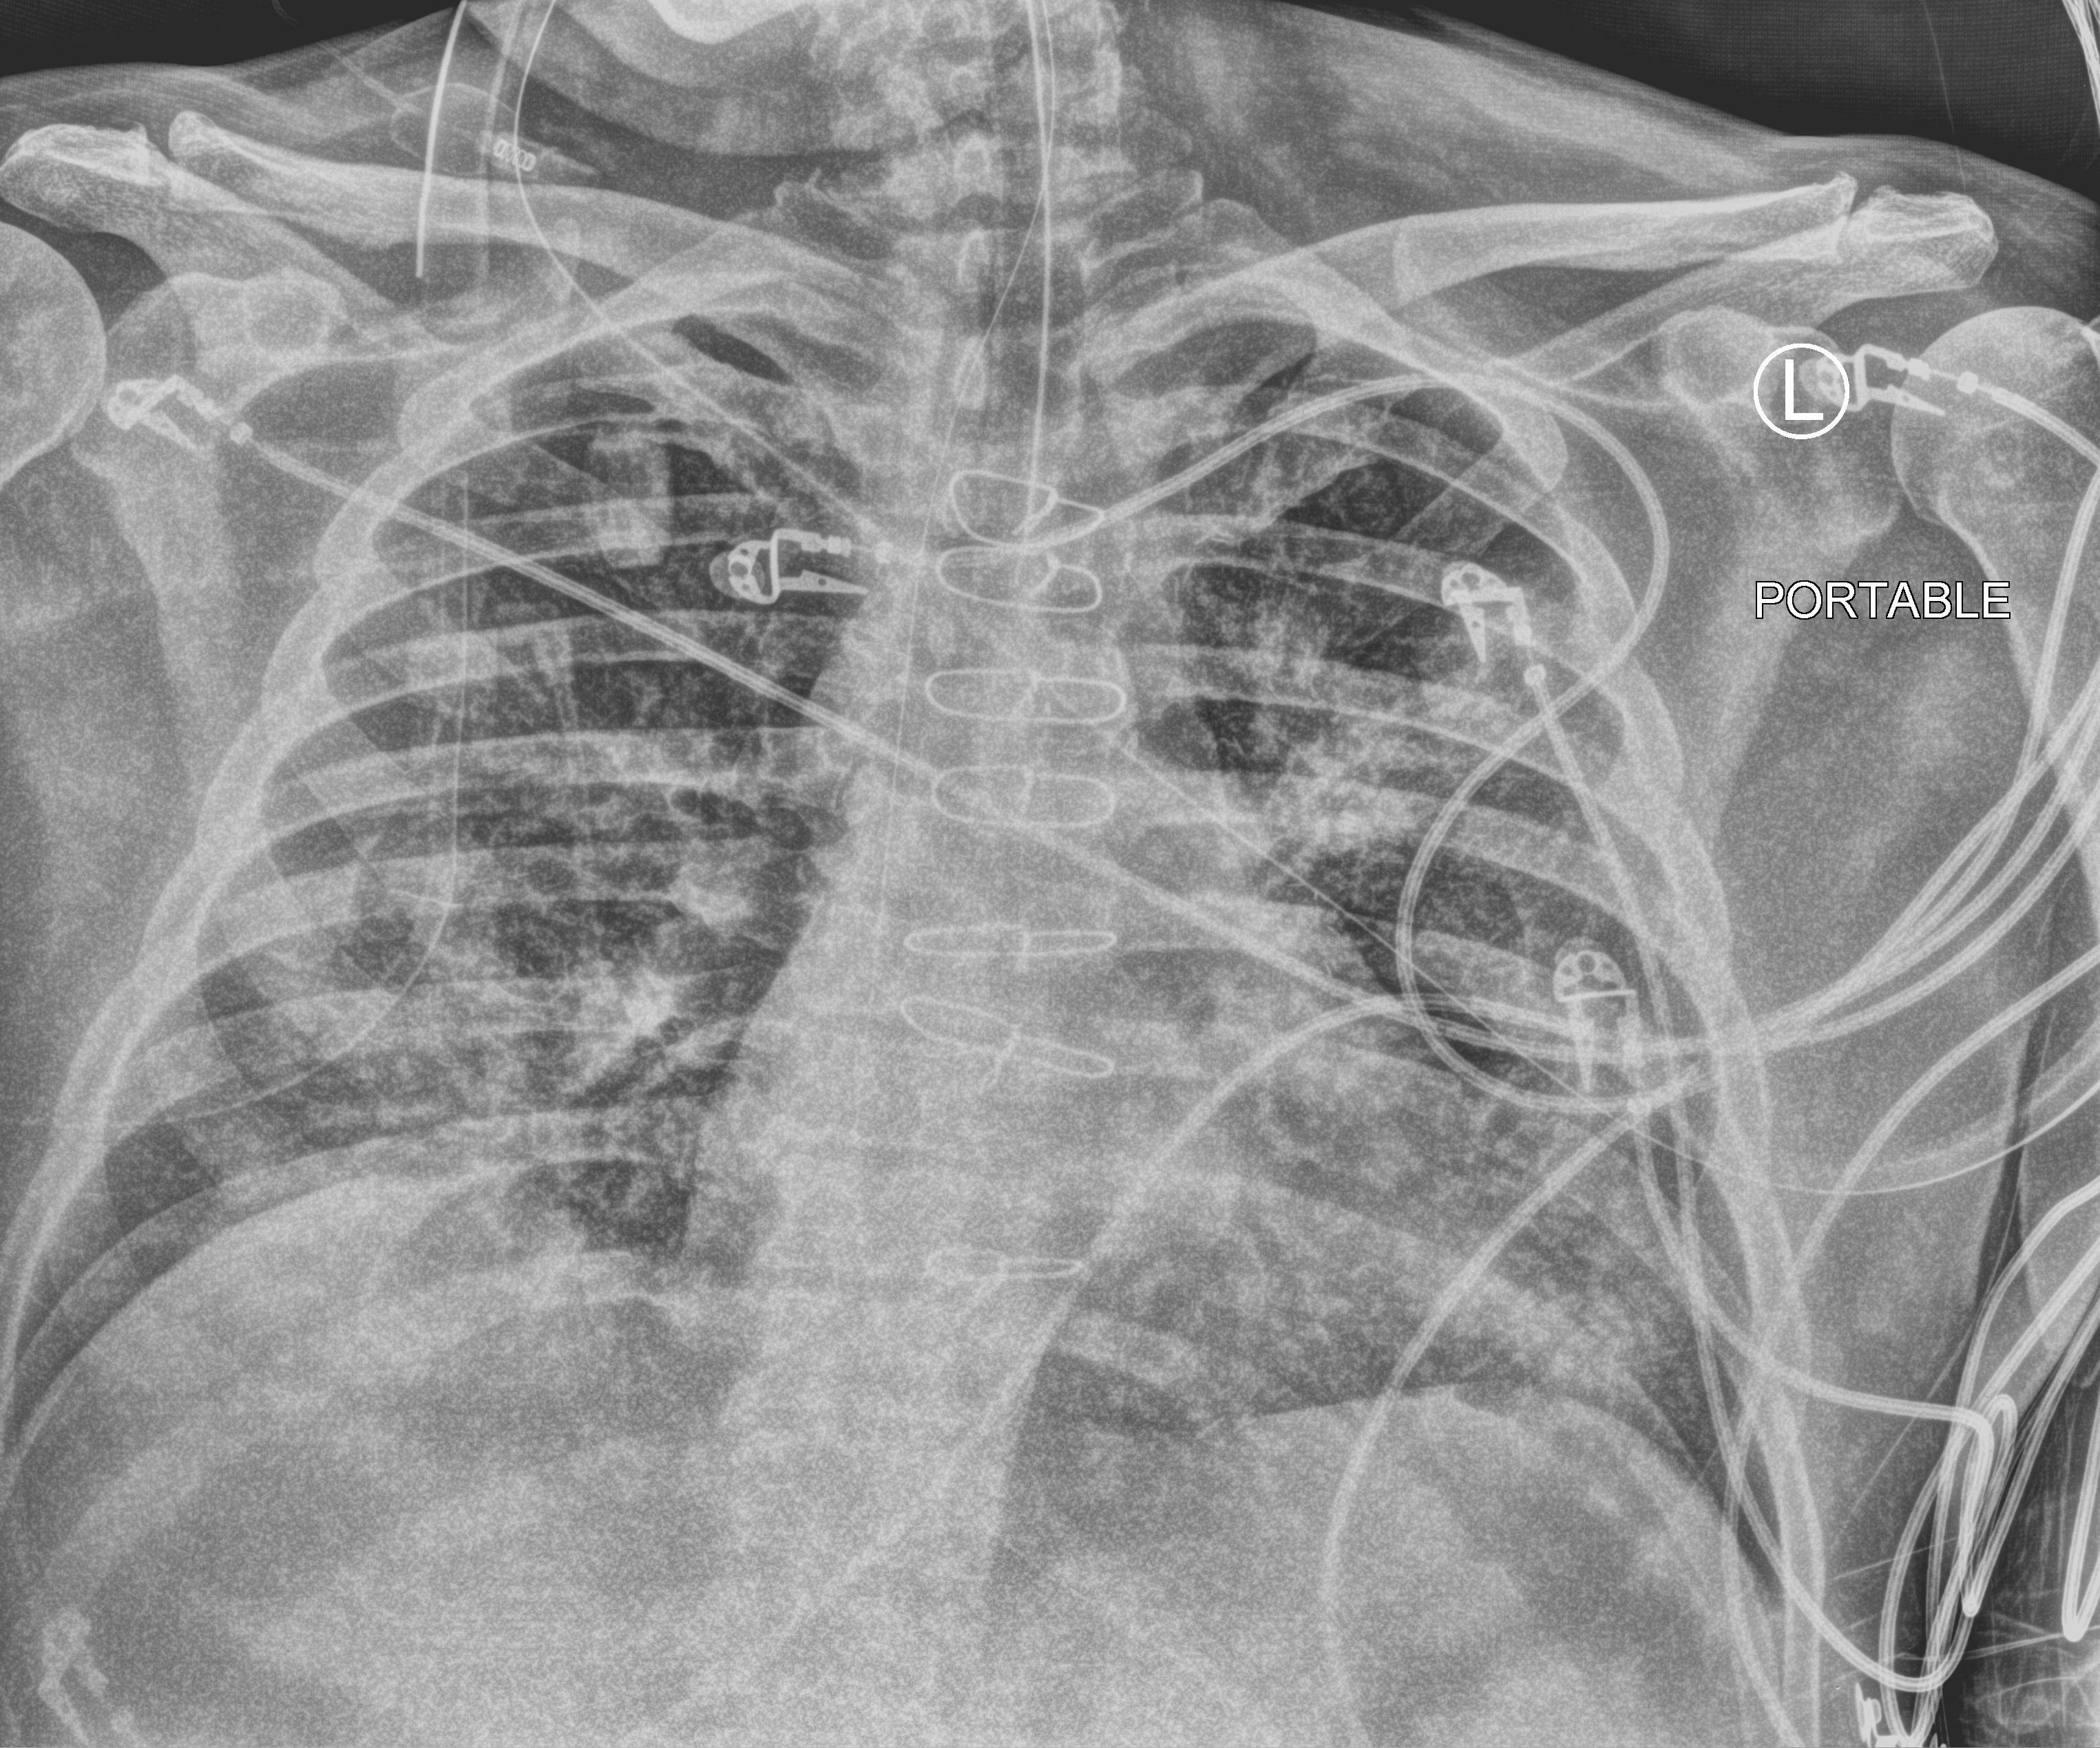
Portable chest radiograph, anteroposterior (AP) projection. Male patient hospitalised with COVID-19, age 60–74 years.
Admission-level facts for this patient (not findings on this image; timing relative to this image not recorded):
- length of hospital stay: 44 days
- COPD (admission record): no
- admitted to intensive care during this hospital stay: yes